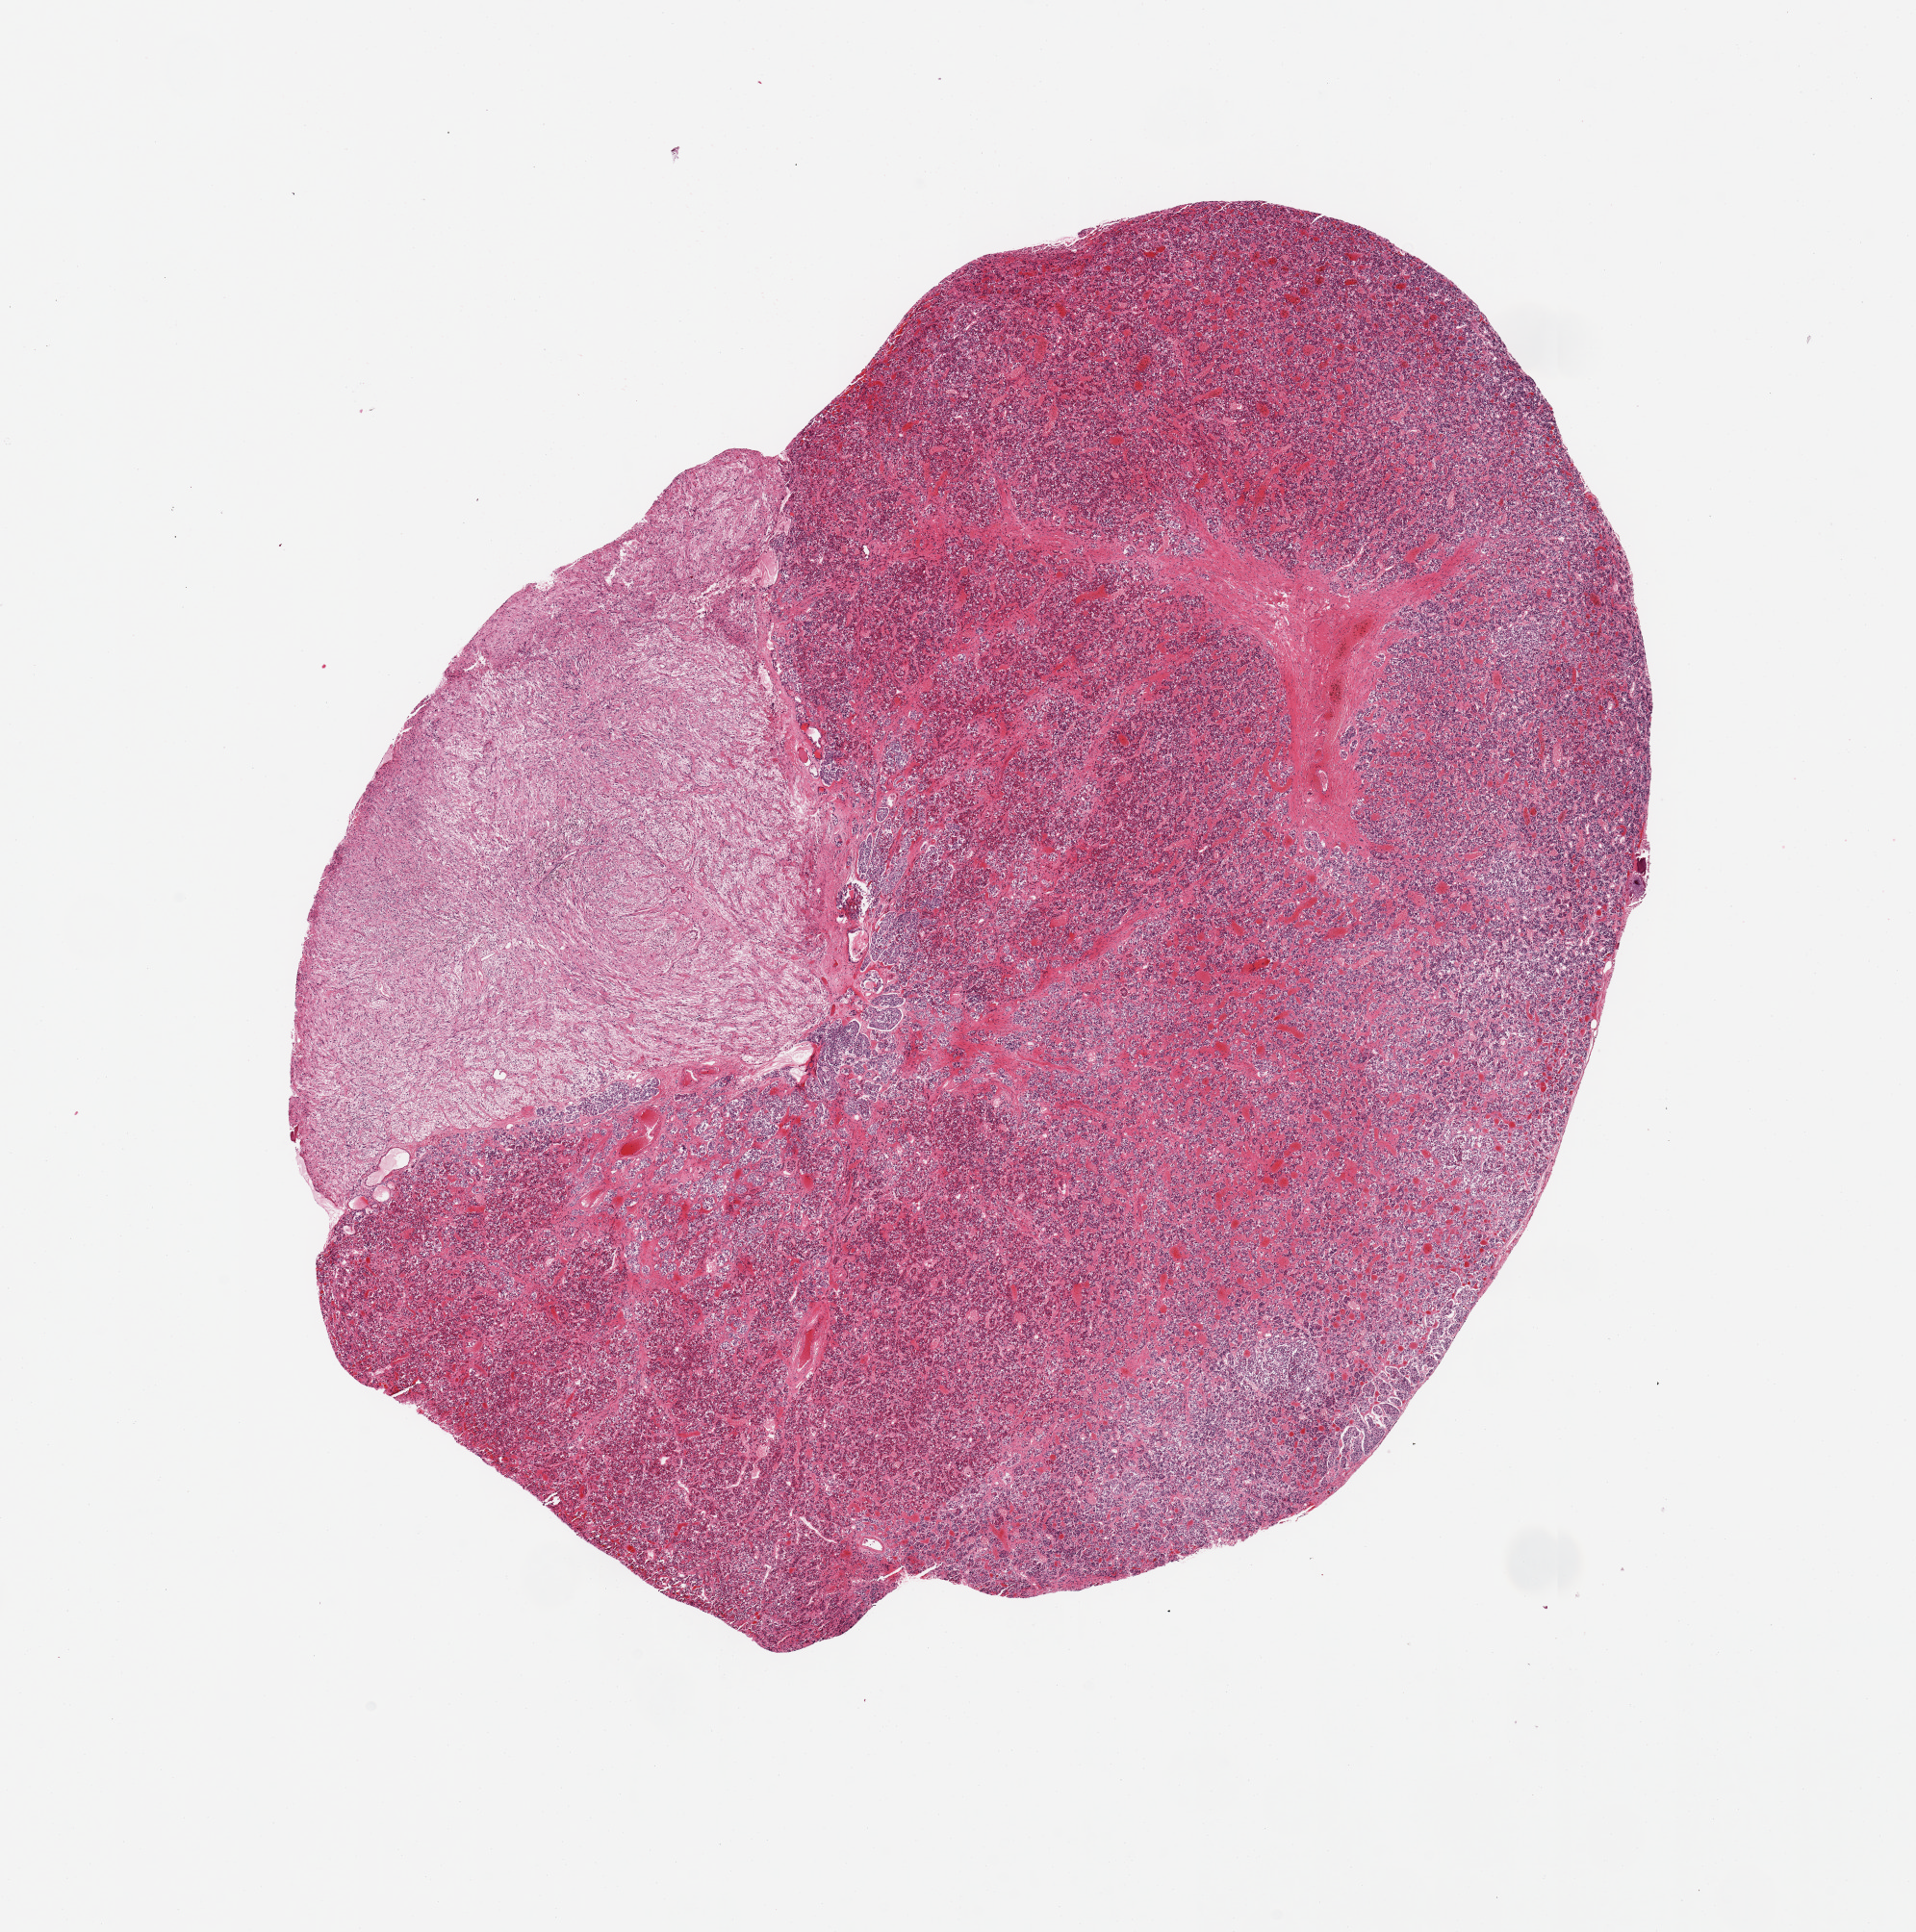
Digitized haematoxylin and eosin-stained section, brightfield — low-resolution overview of the scanned area, about 15.8 x 15.9 mm (acquisition: 20x scan). PAXgene-fixed paraffin-embedded (PFPE) section. Target tissue: pituitary. Tissue donor sample. Donor: male.
- review note (as recorded): 2 pieces, ~30% neurohypophysis, rest adenohypophysis